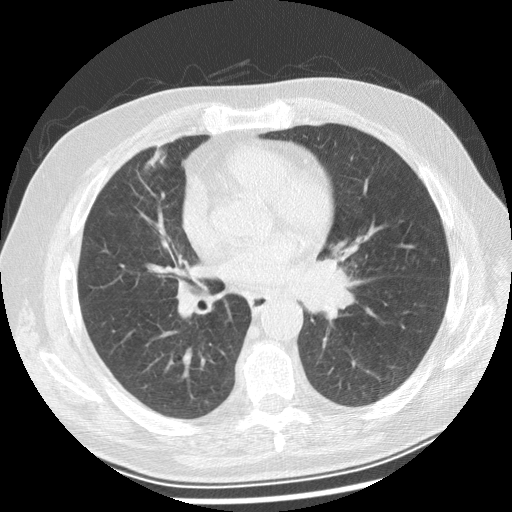
Low-dose screening chest CT, axial slice. First (baseline) screen. Lung window (W 1500 / L -600 HU). Standard (soft-tissue) reconstruction kernel (STANDARD). 120 kVp. Slice 123 of 250 in the series. 512 × 512 image matrix, field of view 360 × 360 mm. Male, age 70 years at enrolment. Current smoker at enrolment.
Lesion marked by an expert reader, bounding box <292,240,376,323> (left, top, right, bottom; pixels). No non-calcified nodule or mass ≥4 mm was recorded by the screening reader at this exam.